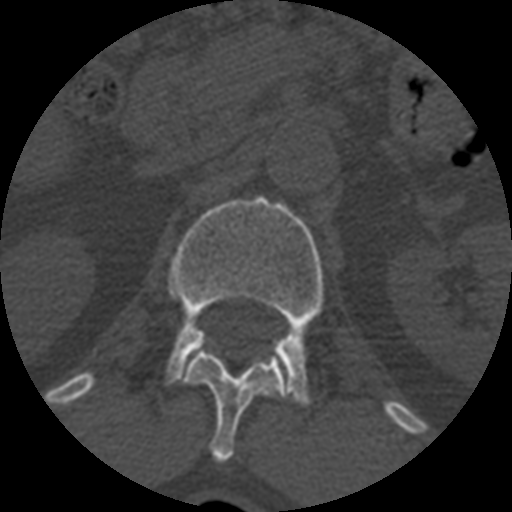
CT including the spine, one axial slice. Slice 371 of 399 in the series (ordered by position). Reconstruction kernel STANDARD. 120 kVp. Bone window (W 1800 / L 400 HU). 512 × 512 image matrix, field of view 160 × 160 mm. Patient age 71 years. From the clinical record (not read from this slice): primary cancer: prostate.
Annotated regions visible in this slice (semi-automatic segmentation, software-assisted and operator-edited):
- L1 vertebra: bounding box <165,197,324,407> (left, top, right, bottom; pixels)
- T12 vertebra: <184,348,290,462>